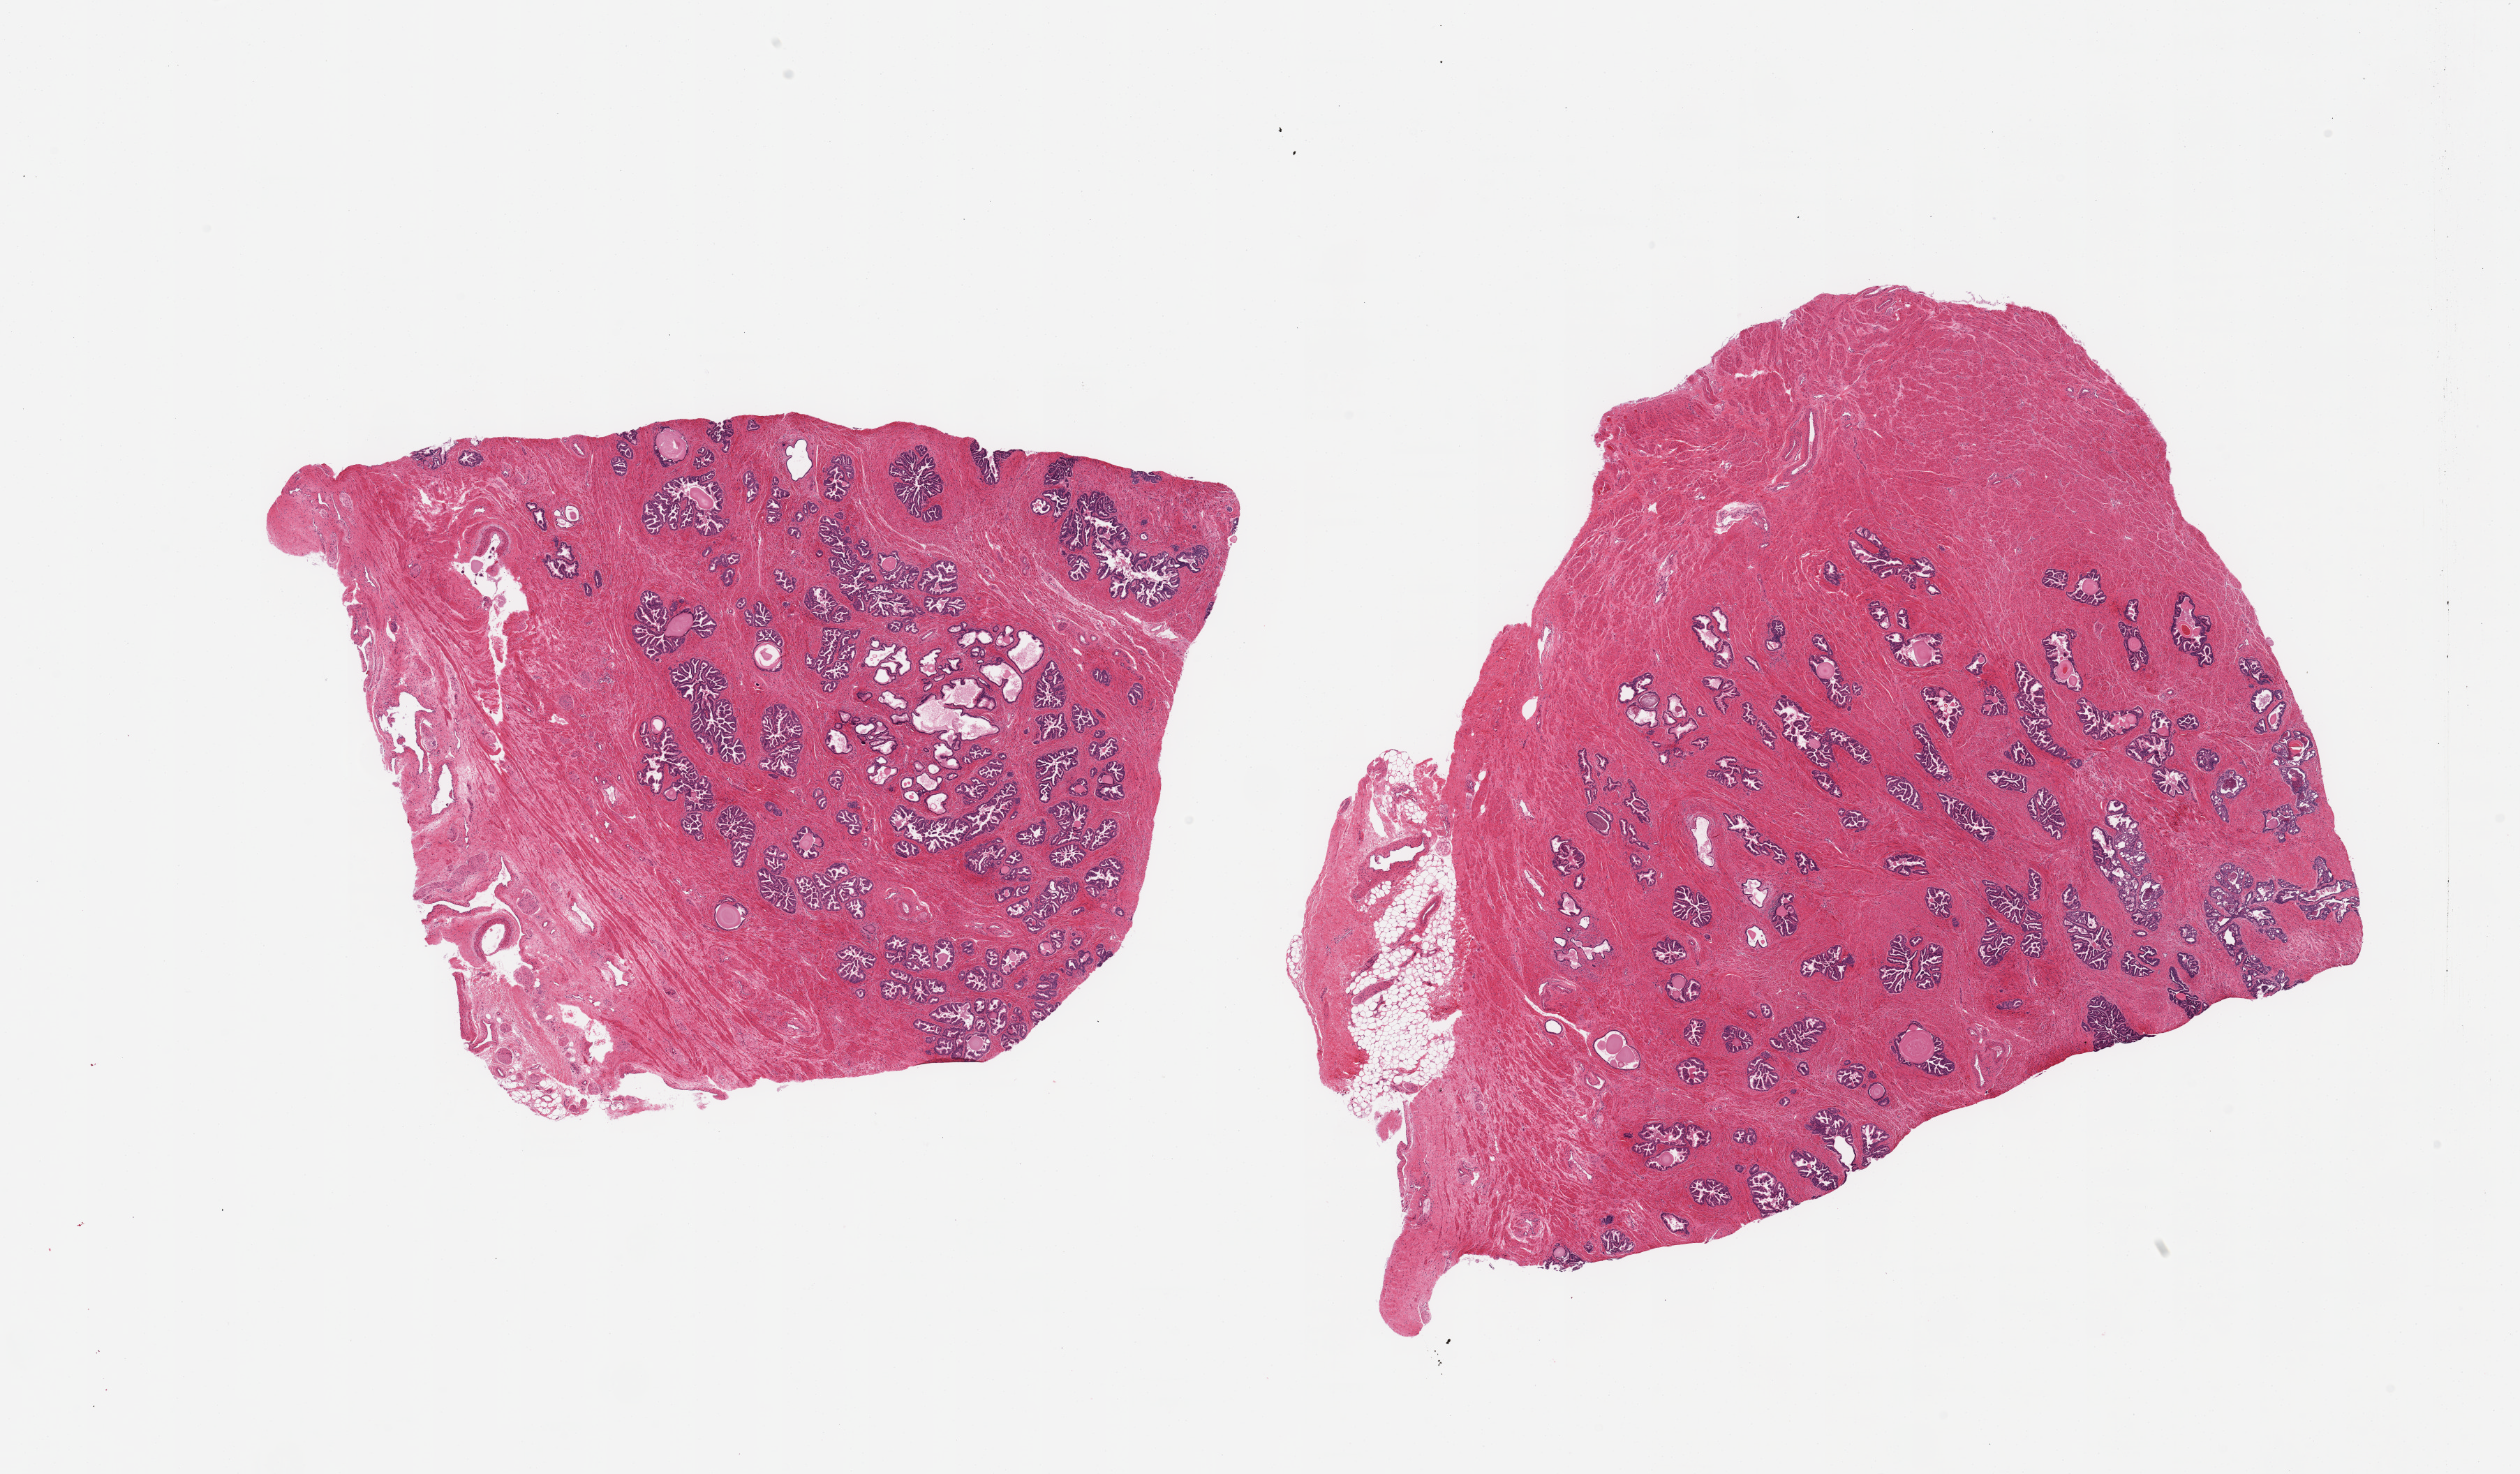
Hematoxylin and eosin (H&E) whole-slide image, shown as a low-resolution overview of the whole scanned area (about 28.5 x 16.7 mm, acquisition: 20x scan), PAXgene-fixed paraffin-embedded (PFPE) section, sampled site (target tissue): prostate, tissue donor sample.
Review note (as recorded): 2 pieces; glandular component and fibromuscular stroma; attached external fat with fibrovascular tissue and nerves.